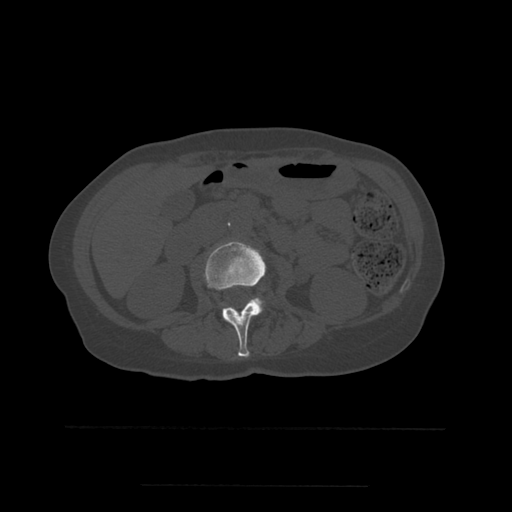
CT including the spine, one axial slice. Position 205 of 544 along the scan axis. Bone window (W 1800 / L 400 HU). 512 × 512 image matrix, field of view 350 × 350 mm. Patient age 58 years. From the clinical record (not read from this slice): primary cancer: lung.
Structures marked on this image (semi-automatic segmentation, software-assisted and operator-edited):
- L2 vertebra: bounding box [x1, y1, x2, y2] px = [204, 242, 266, 358]